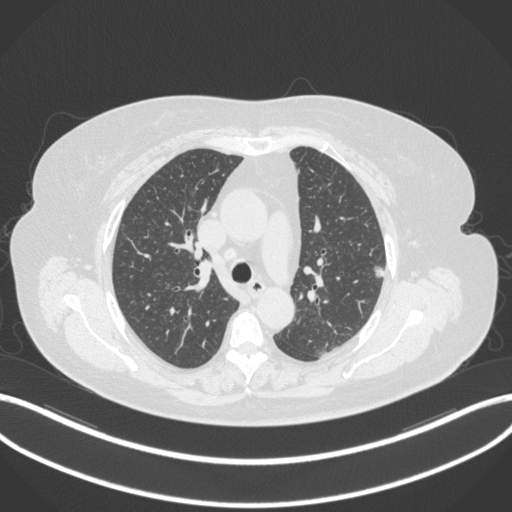
Chest CT, one axial slice. Position 218 of 310 along the scan axis. Reconstruction kernel B31f. 120 kVp. Lung window (W 1500 / L -600 HU). 1 mm slice thickness. 512 × 512 image matrix, field of view 400 × 400 mm. Patient: female, 70 years. Case-level facts recorded for this patient, not image findings: clinical TNM (as recorded): T1c N0 M0.
Structures marked on this image (rectangle marked by the reading radiologist):
- lung tumour (recorded histology: adenocarcinoma): bounding box <367,261,387,281> (left, top, right, bottom; pixels)